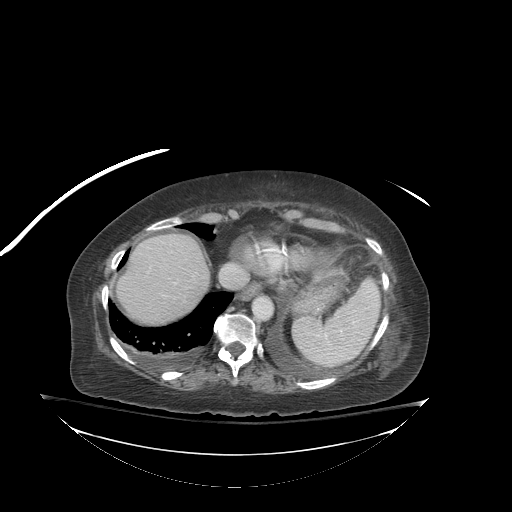
Contrast-enhanced abdominal CT (liver protocol), one axial slice. Position 72 of 81 along the scan axis. Reconstruction kernel STANDARD. 140 kVp. Soft-tissue window (W 400 / L 40 HU). 512 × 512 image matrix, field of view 500 × 500 mm. Case-level facts recorded for this patient, not image findings: diagnosis: hepatocellular carcinoma (patient treated with transarterial chemoembolisation; whether this scan precedes or follows treatment is not stated here); TNM stage (as recorded): Stage-I; Child-Pugh class: B; tumour differentiation: well-moderately differentiated.
Outlined on this slice (semi-automatically segmented with operator editing):
- abdominal aorta: bounding box [x1, y1, x2, y2] px = [254, 298, 272, 320]
- liver parenchyma outside the tumour (the mass and vessels are separate outlines, so this box may not span the whole liver): [126, 234, 209, 320]